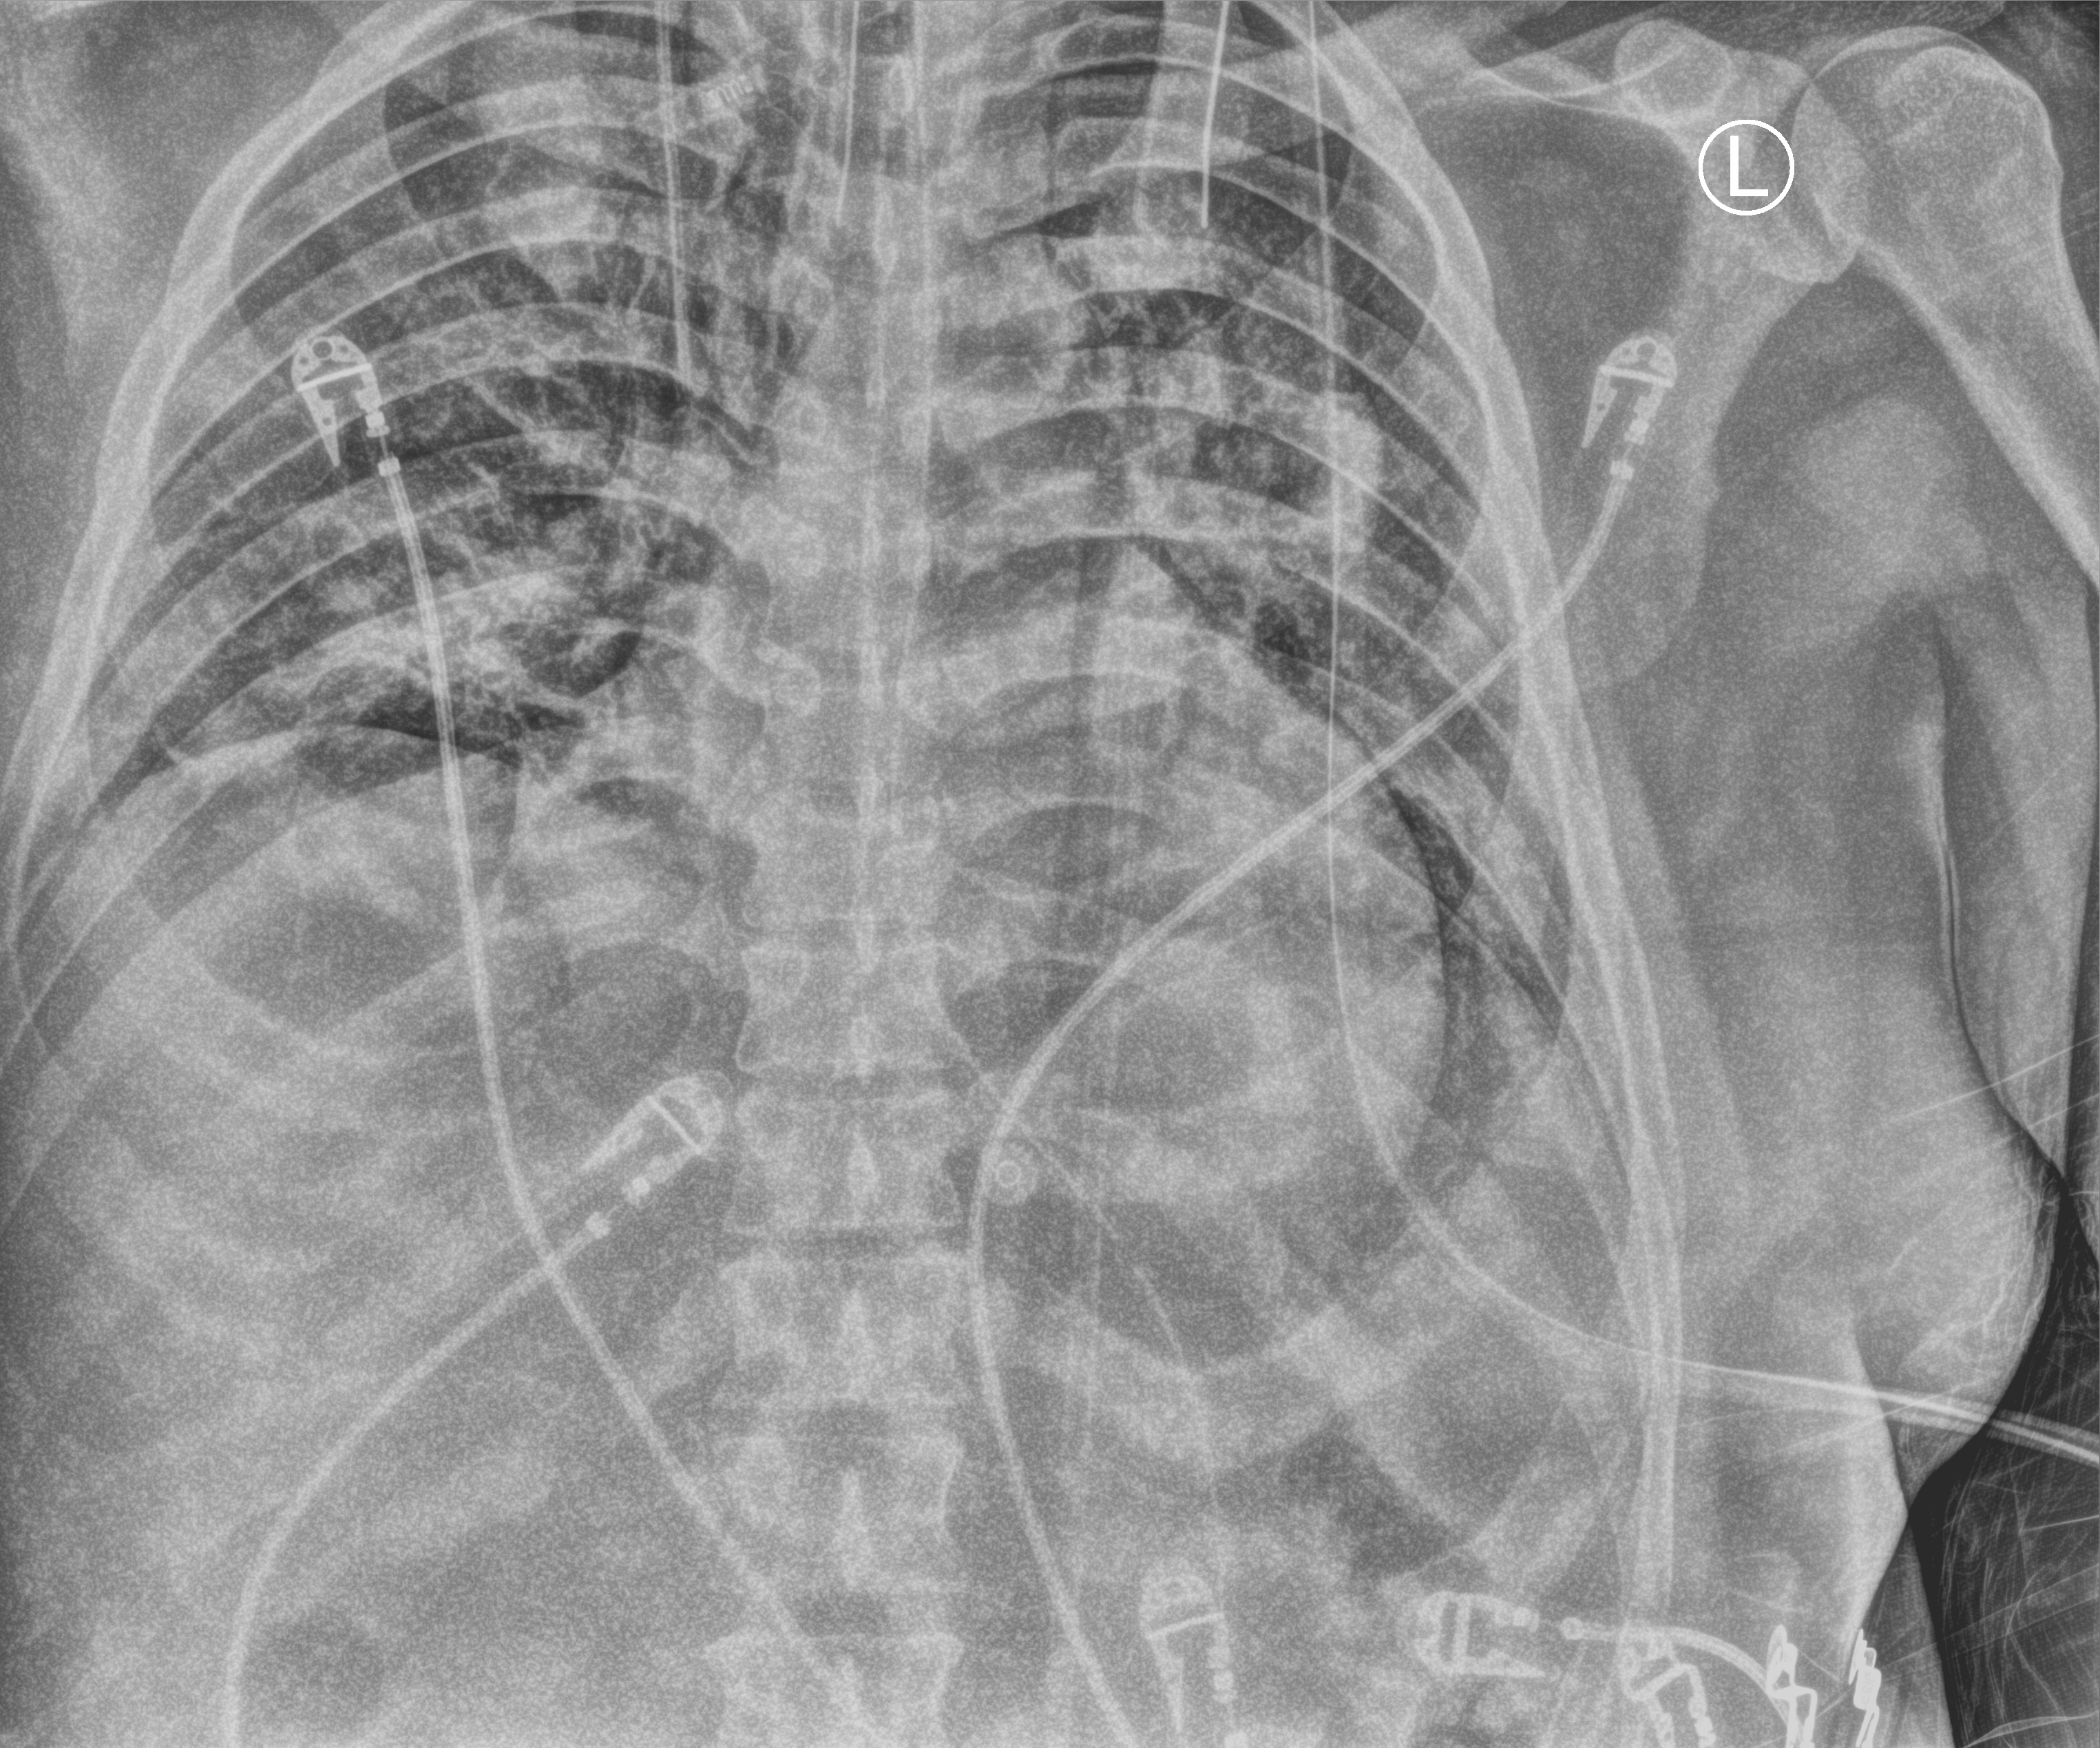
Chest X-ray (portable); anteroposterior (AP) projection. Patient hospitalised with COVID-19; male, aged 18–59 years.
Admission-level facts for this patient (not findings on this image; timing relative to this image not recorded):
- admitted to intensive care during this hospital stay: yes
- mechanically ventilated during this hospital stay: yes